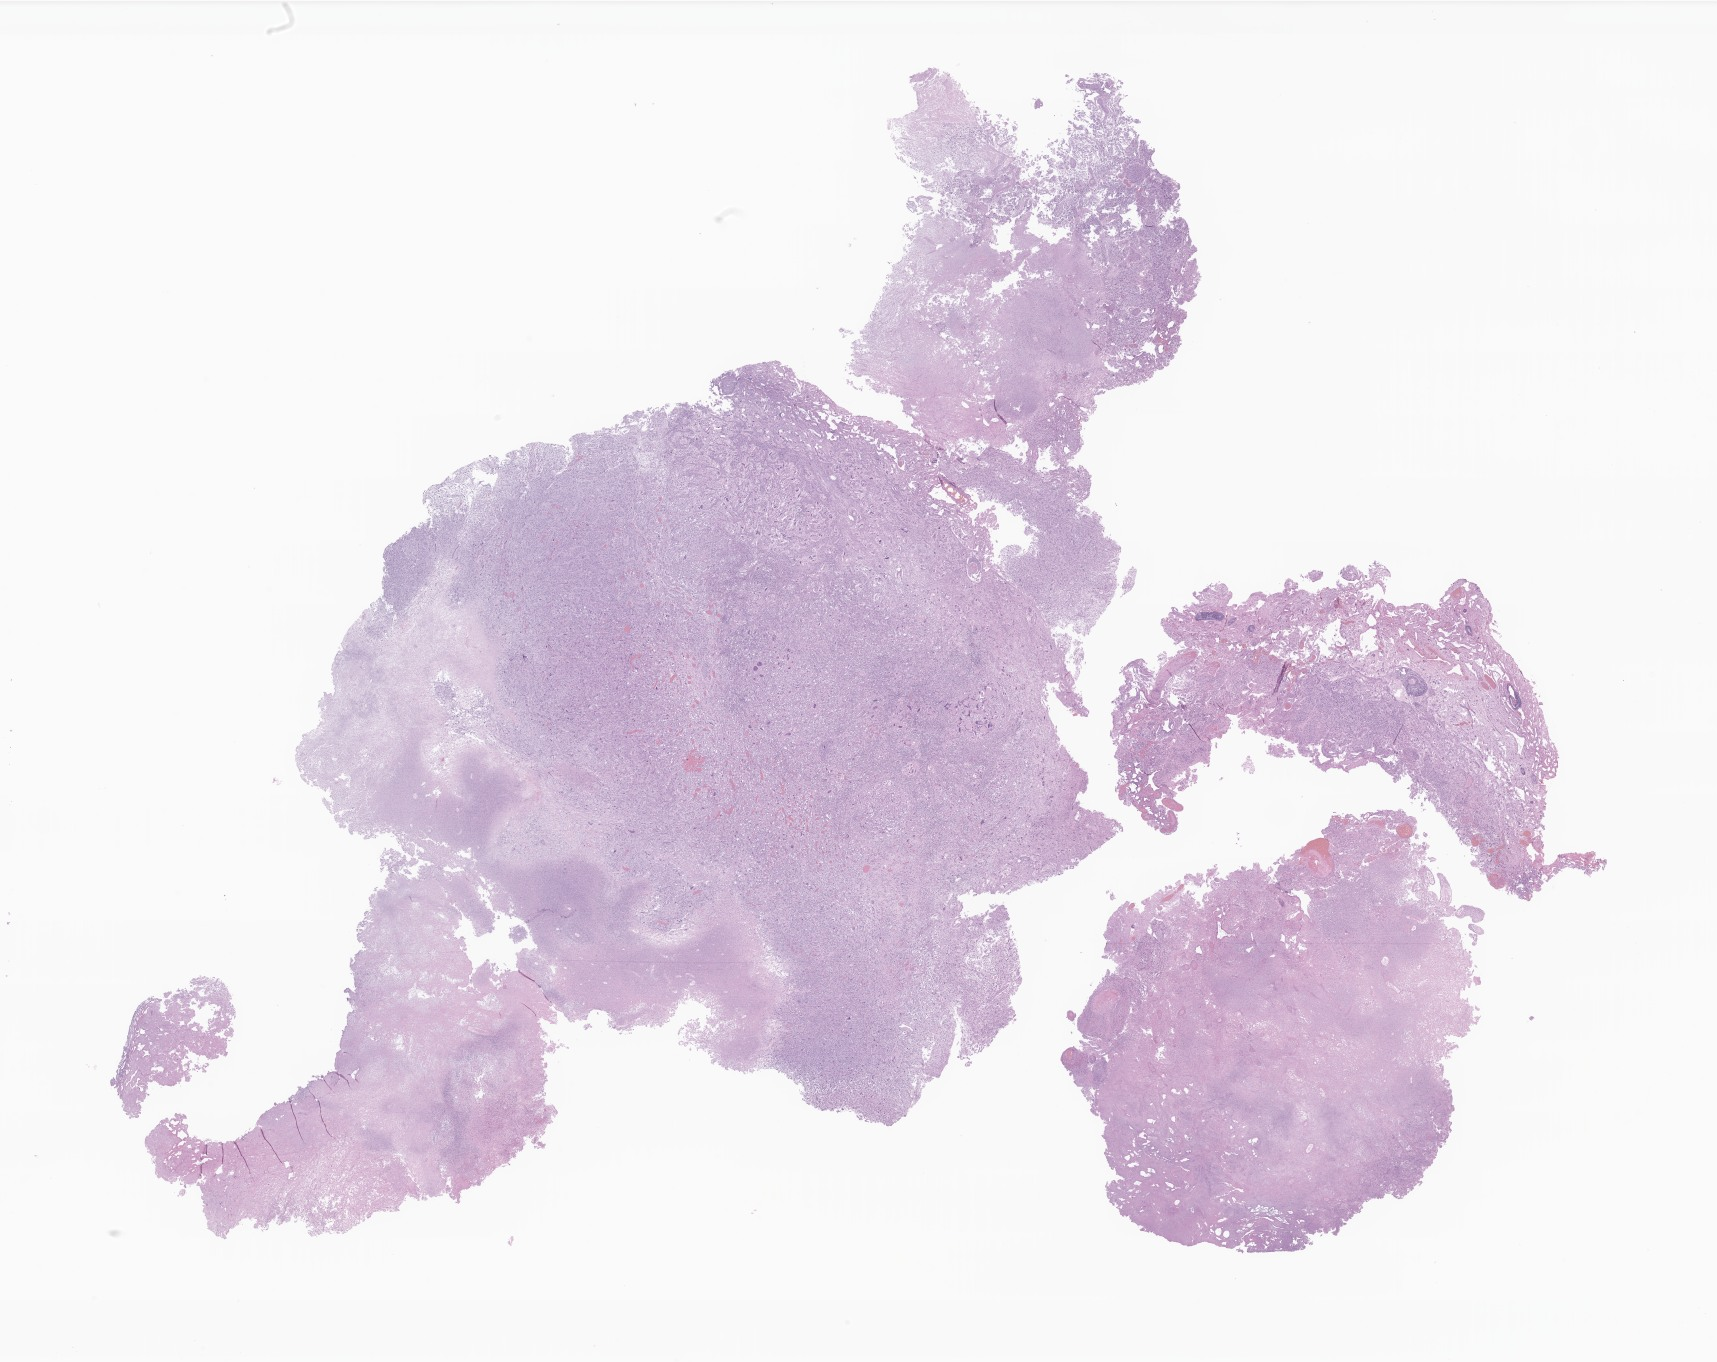
Digitized H&E-stained section of tumor tissue from the frontal lobe — whole scanned area (about 29.0 x 23.0 mm) shown as a low-resolution overview. Formalin-fixed, paraffin-embedded (FFPE) tissue. Male patient, age 207 months.
Recorded diagnosis: Glioblastoma, NOS.